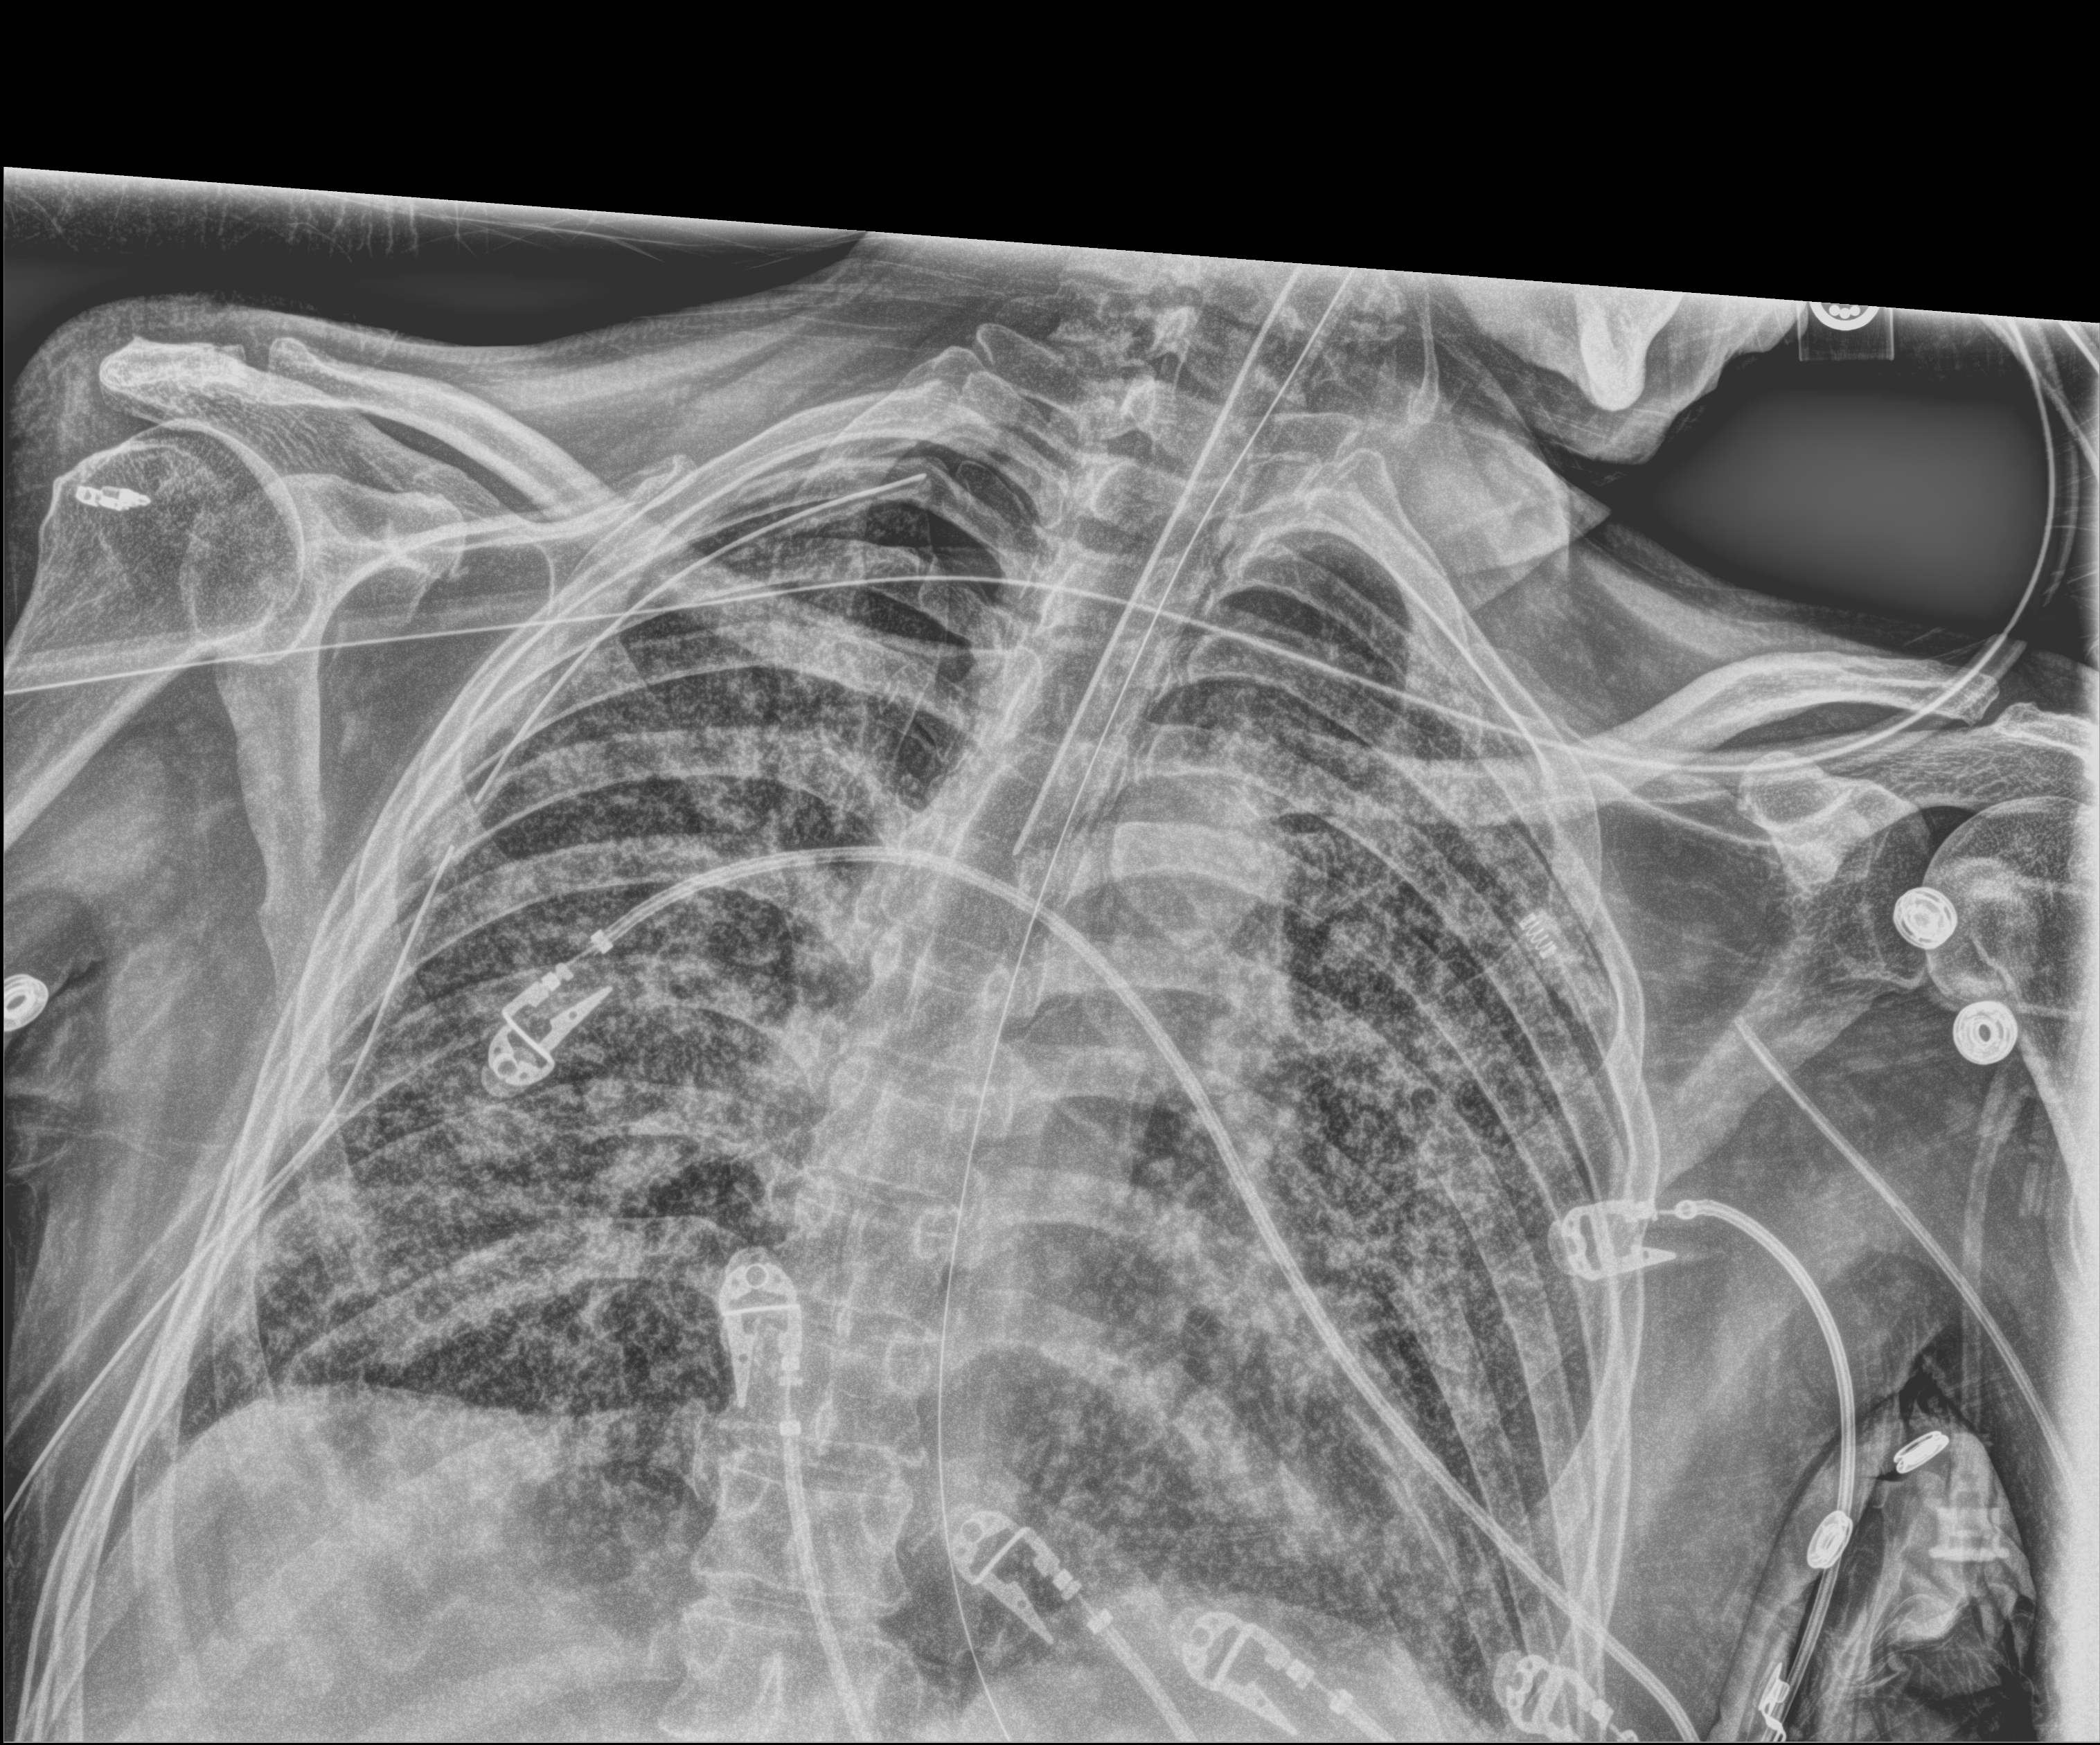
Portable chest radiograph, anteroposterior (AP) projection. Patient hospitalised with COVID-19; male, aged 60–74 years.
Hospital-stay facts (about this admission, not read from this image; timing relative to this image not recorded): admitted to intensive care during this hospital stay: yes; mechanically ventilated during this hospital stay: yes.